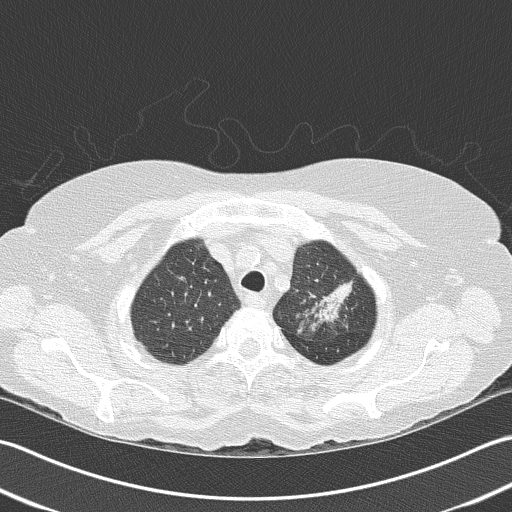
Chest CT (low-dose screening protocol), one axial image, baseline annual screen, lung window (W 1500 / L -600 HU), 120 kVp, 512 × 512 image matrix. Female, age 68 years at enrolment. Former smoker at enrolment.
Lesion marked by an expert reader, bounding box (x1, y1, x2, y2) in pixels: (292, 259, 366, 331). No non-calcified nodule or mass ≥4 mm was recorded by the screening reader at this exam. Official screen result: negative screen, minor abnormalities not suspicious for lung cancer. Participant outcome: lung cancer diagnosed 763 days after this screen — adenocarcinoma, NOS, left upper lobe, poorly differentiated (G3), stage IB (AJCC 6th edition), 50 mm at pathology.